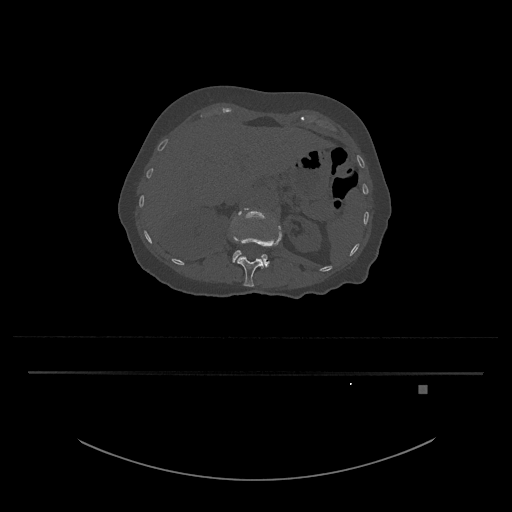
CT including the spine, one axial slice. Slice 533 of 797 in the series (ordered by position). Reconstruction kernel Br40s/3. 120 kVp. Bone window (W 1800 / L 400 HU). 0.5 mm slice thickness. 512 × 512 image matrix. Patient: female, 57 years. From the clinical record (not read from this slice): primary cancer: cervical.
Outlined on this slice (semi-automatic segmentation, software-assisted and operator-edited):
- L1 vertebra: bounding box (x1, y1, x2, y2) in pixels: (232, 221, 282, 287)